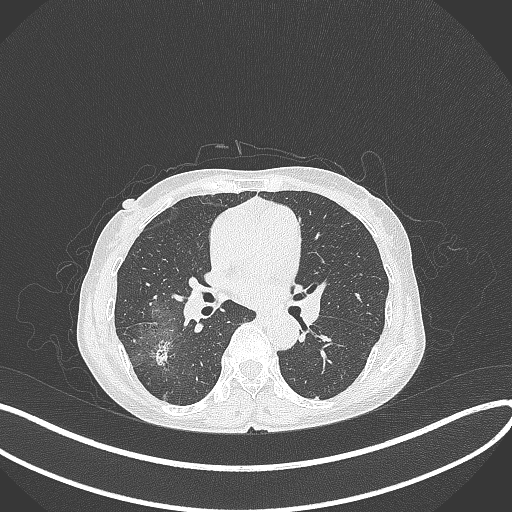
Chest CT, one axial slice. Lung window (W 1500 / L -600 HU). 1 mm slice thickness. 512 × 512 image matrix. Patient: female, 69 years. Case-level facts recorded for this patient, not image findings: clinical TNM (as recorded): T1b N0 M0.
Structures marked on this image (bounding box drawn by a radiologist):
- lung tumour (recorded histology: adenocarcinoma): bounding box (x1, y1, x2, y2) in pixels: (151, 335, 176, 370)